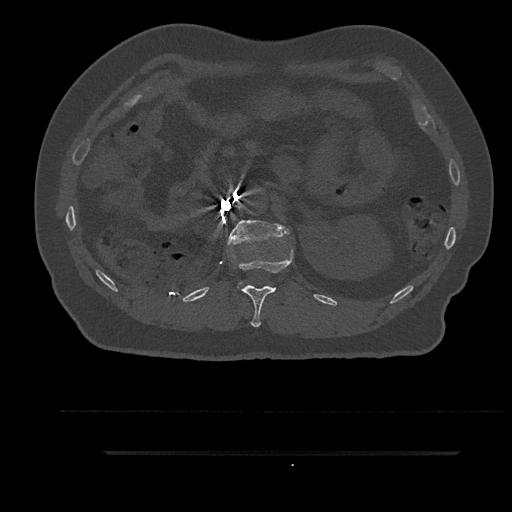
CT including the spine, one axial slice. Position 217 of 797 along the scan axis. Reconstruction kernel Br40s/3. 120 kVp. Bone window (W 1800 / L 400 HU). 512 × 512 image matrix. Patient: male, 63 years. Case-level facts recorded for this patient, not image findings: primary cancer: renal; vertebrae with lytic lesions (as recorded): T8.
Annotated regions visible in this slice (semi-automatically segmented with operator editing):
- L1 vertebra: bounding box <227,219,290,287> (left, top, right, bottom; pixels)
- T12 vertebra: <238,249,294,327>